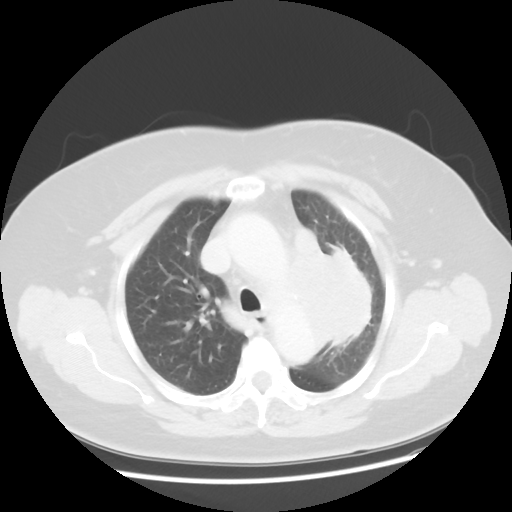
Chest CT, one axial slice; slice 34 of 49 in the series (ordered by position); 120 kVp; lung window (W 1500 / L -600 HU); 512 × 512 image matrix. Female patient, age 58 years. From the clinical record (not read from this slice): clinical TNM (as recorded): T4 N3 M0.
Annotated regions visible in this slice (rectangle marked by the reading radiologist):
- lung tumour (recorded histology: small cell carcinoma): bounding box [x1, y1, x2, y2] px = [291, 224, 381, 362]